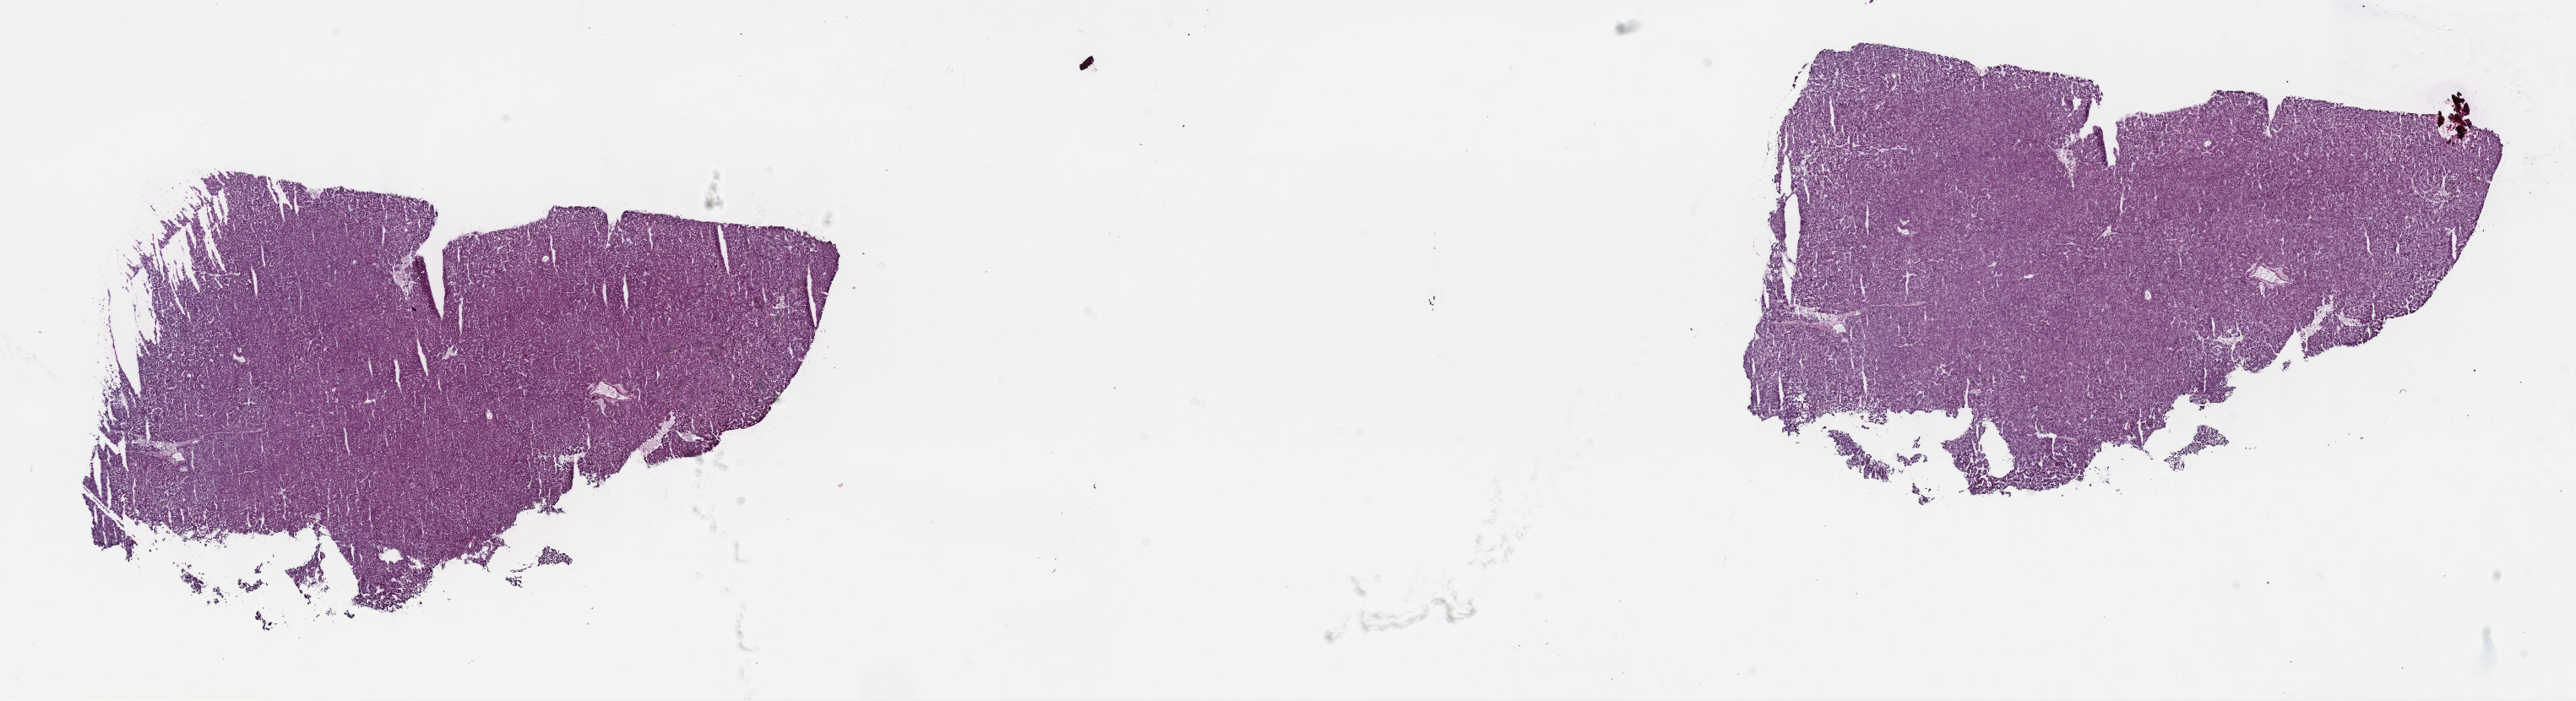
Digitized H&E tissue section (whole slide) — a low-resolution overview of the entire scanned area, about 24.7 x 6.7 mm (slide scanned at 40x); frozen section; liver, primary tumour sample. Patient: male, age at initial diagnosis 65 years. Histologic grade: G3 (poorly differentiated). Slide review estimates, as recorded: tumour cells 80%, tumour nuclei 80%, normal cells 0%, stromal cells 20%, necrosis 0%. Infiltration values recorded for this section: lymphocyte infiltration 3%, monocyte infiltration 1%, neutrophil infiltration 2%.
* AJCC pathologic stage: I (6th edition)
* pathologic diagnosis: Hepatocellular carcinoma, NOS